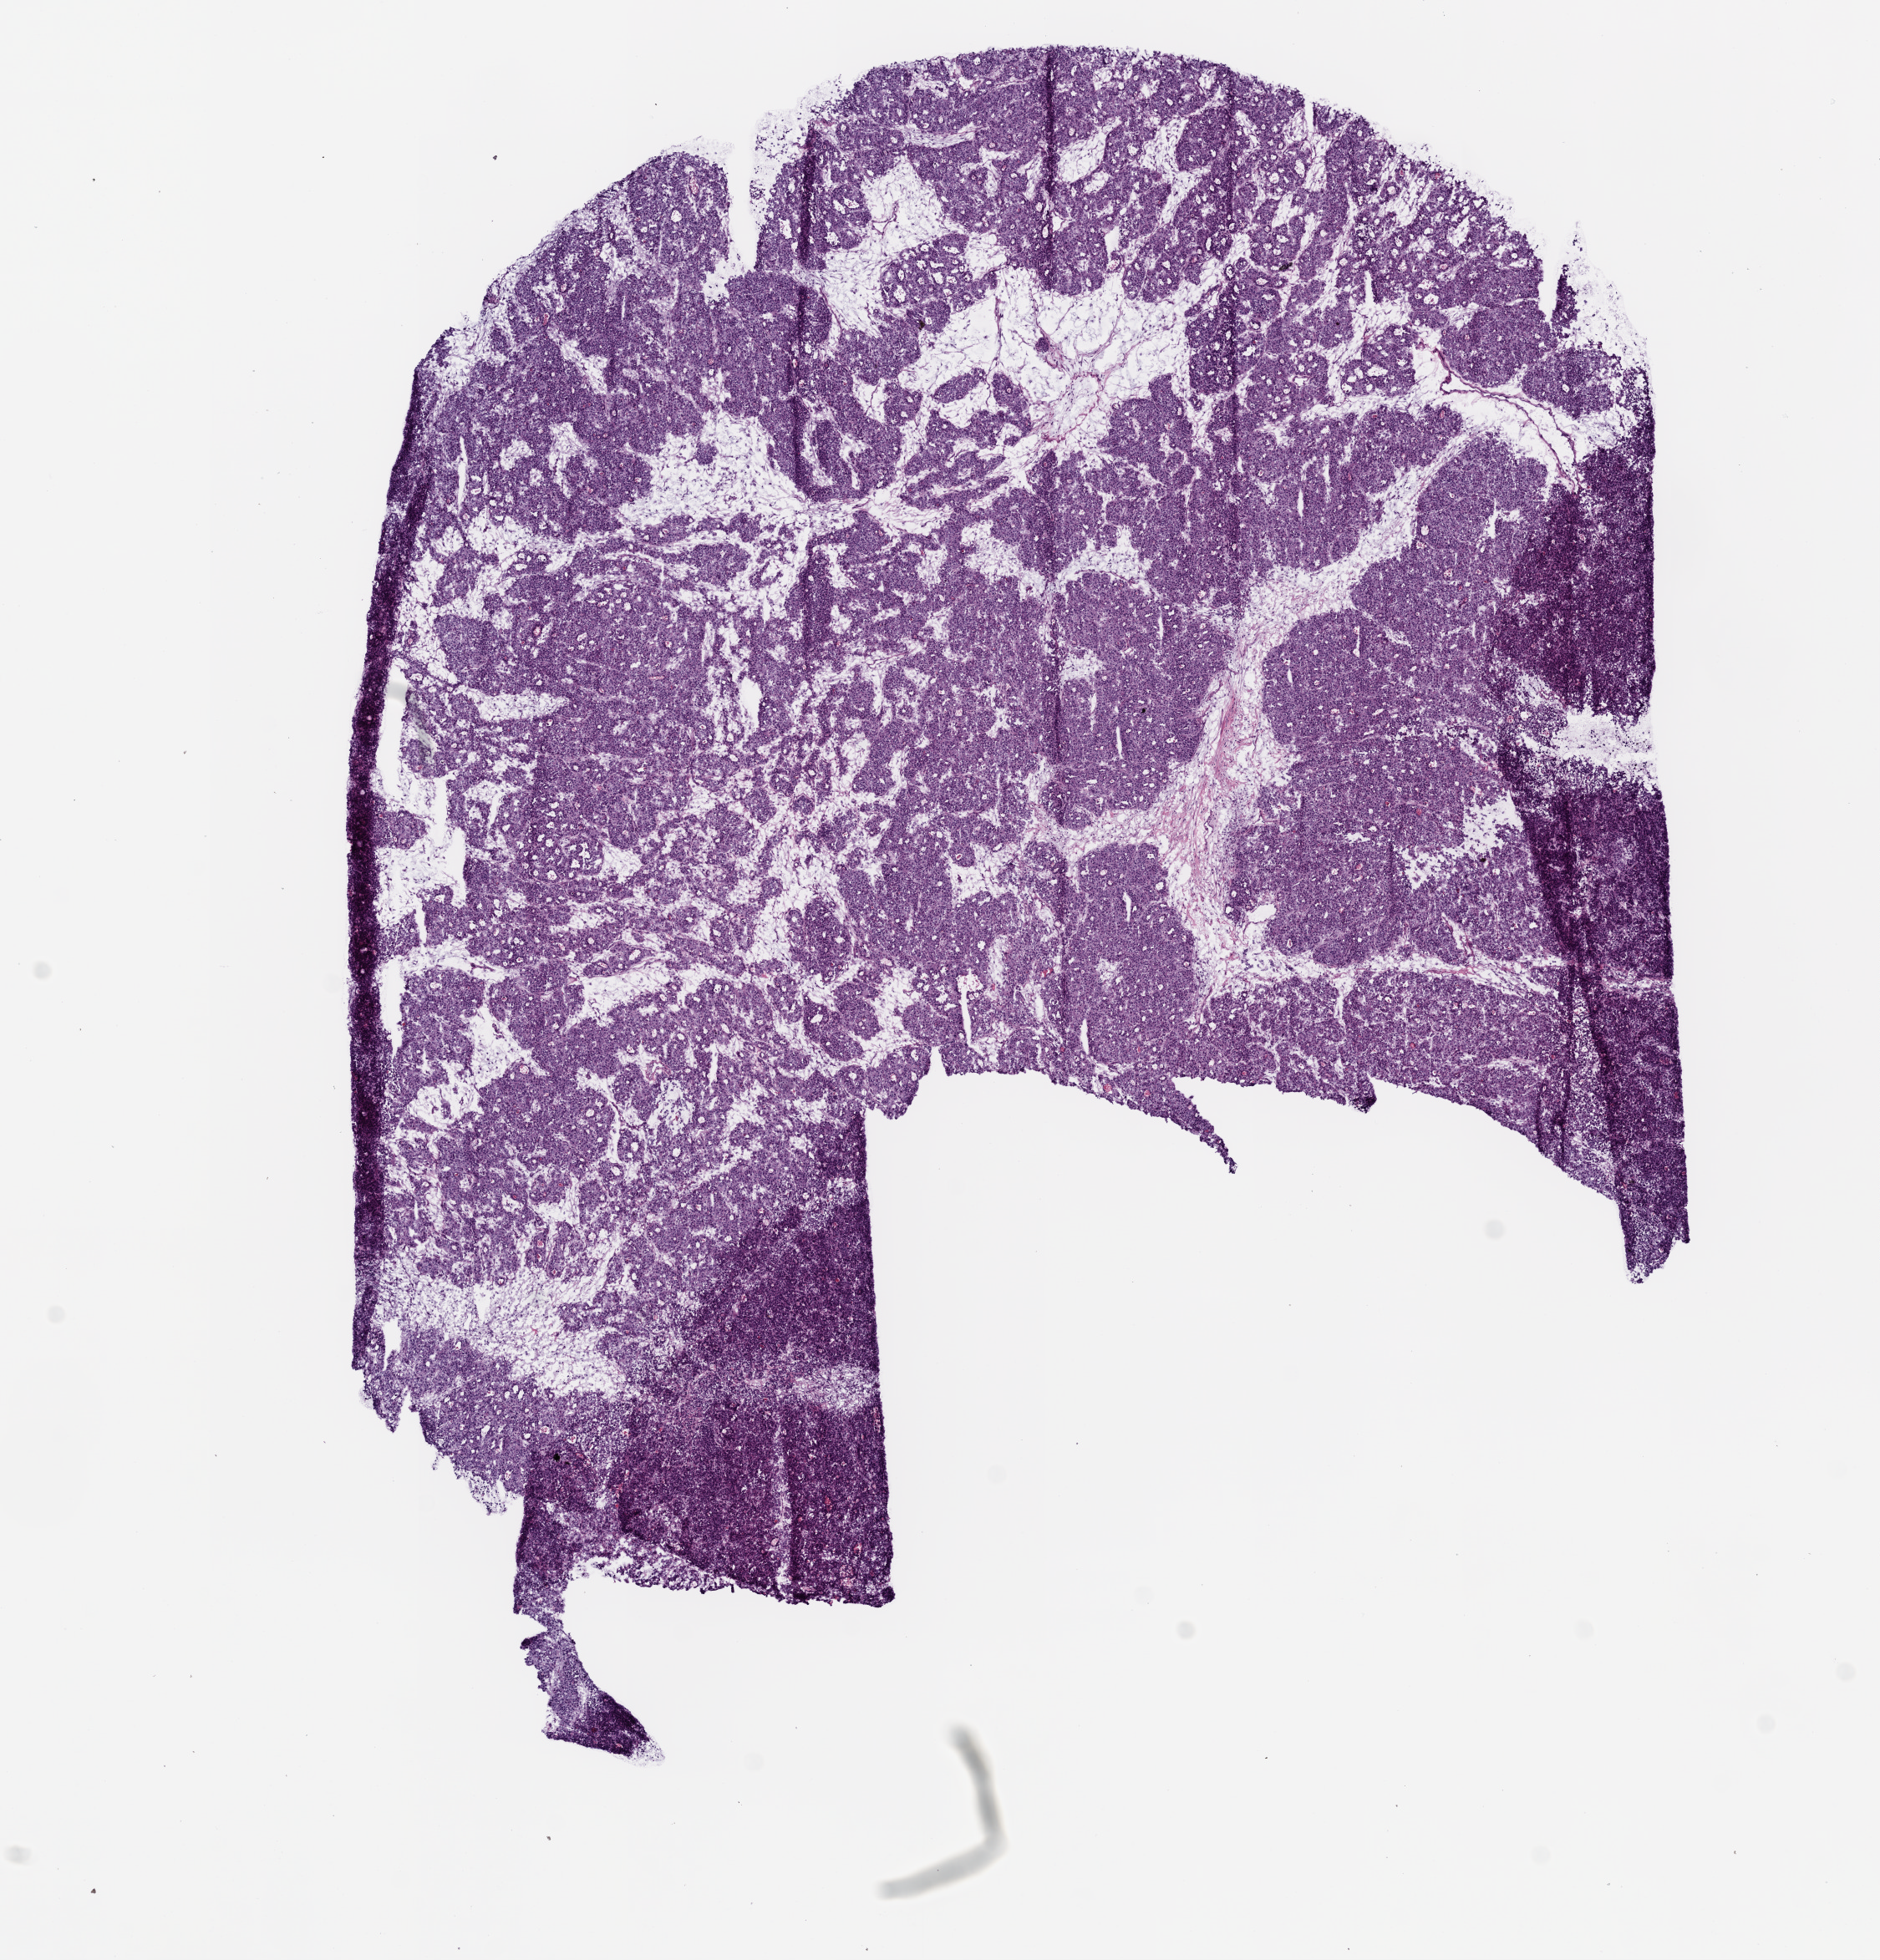
Digitized H&E-stained tissue section (whole slide) — shown as a low-resolution overview of the whole scanned area (about 9.0 x 9.4 mm, slide scanned at 20x); frozen section from the bottom of the tissue portion; sample: primary tumour, stomach. Male patient; age at initial diagnosis 68 years. Histologic grade: G2 (moderately differentiated). Composition of this section per pathologist review: tumour cells 87%, tumour nuclei 80%, normal cells 0%, stromal cells 10%, necrosis 3%.
Histologic diagnosis: Adenocarcinoma, intestinal type. AJCC pathologic stage: IA (5th edition).